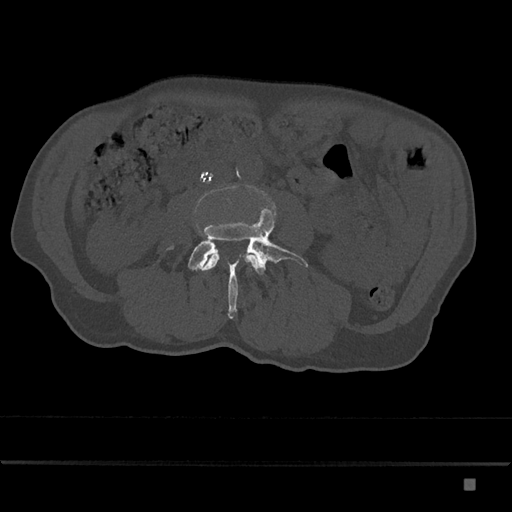
CT including the spine, one axial slice; slice 360 of 797 in the series (ordered by position); bone window (W 1800 / L 400 HU); 512 × 512 image matrix, field of view 390 × 390 mm. Male patient, age 72 years. Case-level facts recorded for this patient, not image findings: primary cancer: prostate.
Annotated regions visible in this slice (semi-automatically segmented with operator editing):
- L3 vertebra: bounding box (x1, y1, x2, y2) in pixels: (202, 253, 259, 271)
- L4 vertebra: (169, 208, 308, 319)